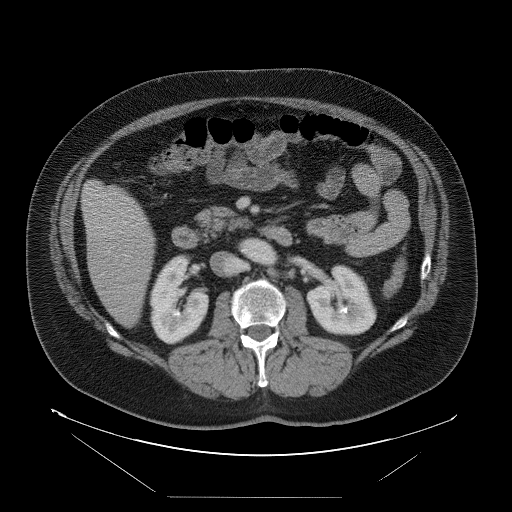
Contrast-enhanced abdominal CT, one axial slice. Intravenous contrast given. Soft-tissue window (W 400 / L 40 HU). 512 × 512 image matrix, field of view 500 × 500 mm. Male patient, age 61 years. From the clinical record (not read from this slice): diagnosis: colorectal cancer liver metastases, imaged before liver resection; multiple liver metastases: no; largest metastasis: 6.5 cm; chemotherapy before resection: no.
Structures marked on this image (manually delineated by an expert):
- liver: bounding box [x1, y1, x2, y2] px = [83, 181, 156, 327]